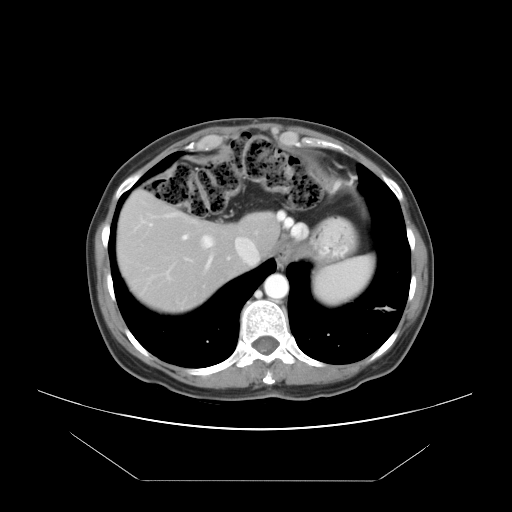
Contrast-enhanced abdominal CT, one axial slice; slice 37 of 45 in the series (ordered by position); reconstruction kernel STANDARD; 120 kVp; intravenous contrast given; soft-tissue window (W 400 / L 40 HU); 512 × 512 image matrix, field of view 405 × 405 mm. Female patient, age 52 years. Case-level facts recorded for this patient, not image findings: diagnosis: colorectal cancer liver metastases, imaged before liver resection; multiple liver metastases: yes; largest metastasis: 2.5 cm; disease in both lobes: no.
Outlined on this slice (expert manual segmentation):
- hepatic veins: bounding box (x1, y1, x2, y2) in pixels: (148, 212, 215, 283)
- liver: (118, 192, 276, 312)
- planned liver remnant (the part of the liver to remain after resection): (118, 192, 276, 294)
- portal vein (with intrahepatic branches): (150, 224, 188, 240)